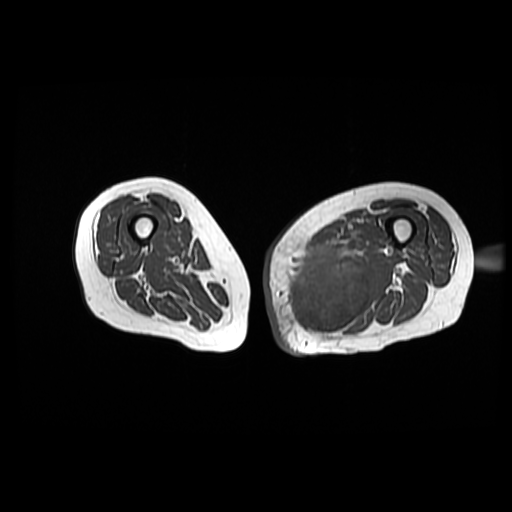
MRI of an extremity soft-tissue mass, one axial slice. Slice 34 of 42 in the series (ordered by position). 512 × 512 image matrix, field of view 420 × 420 mm. Female patient. From the clinical record (not read from this slice): histological type: pleomorphic leiomyosarcoma; grade: high; site of the primary tumour: left thigh.
Outlined on this slice (manually delineated by an expert):
- gross tumour volume including surrounding oedema: bounding box [x1, y1, x2, y2] px = [290, 243, 377, 335]
- gross tumour volume (mass): [290, 243, 371, 337]